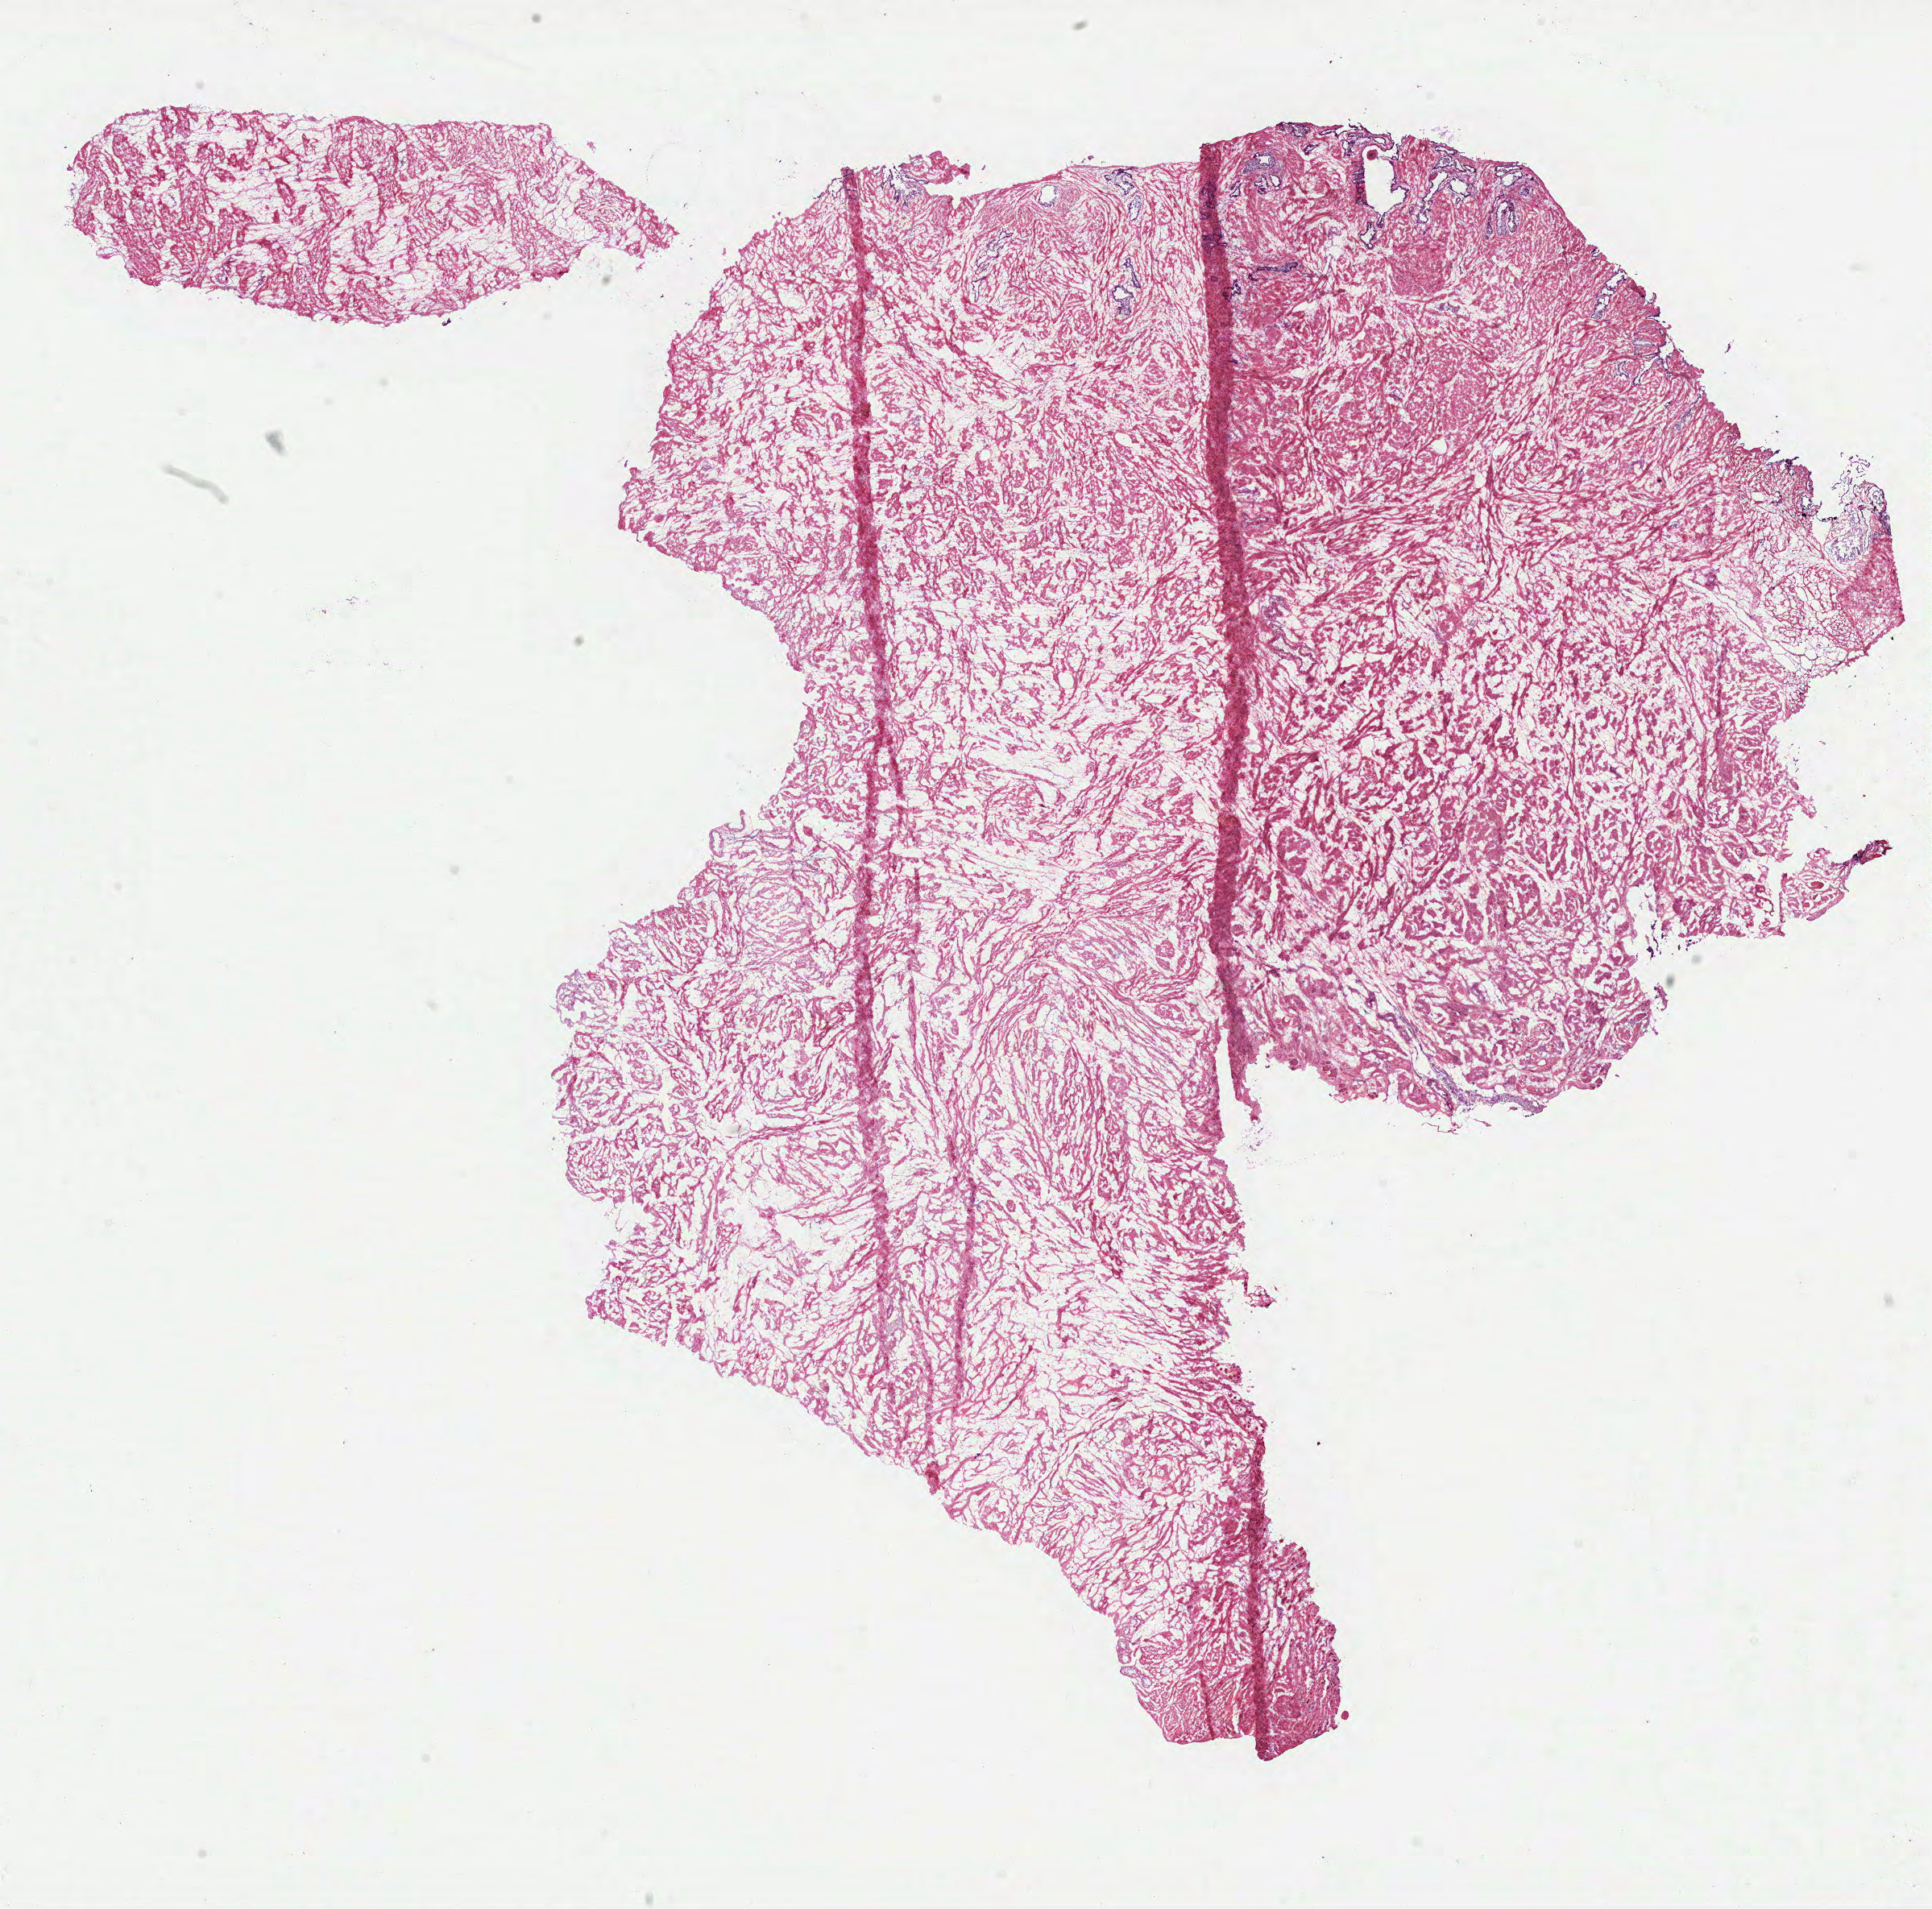
Whole-slide histology image, Hematoxylin and eosin (H&E) stained, low-resolution overview of the scanned area, about 19.3 x 19.1 mm, frozen section, sample: solid tissue normal (non-tumour tissue), prostate. Patient: male, age at initial diagnosis 70 years.
This section: solid tissue normal (non-tumour) sample from the same patient. Patient diagnosis: Acinar cell carcinoma.